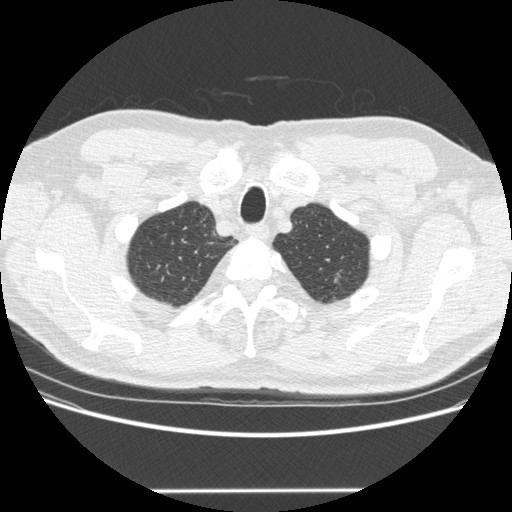
Low-dose screening chest CT, axial slice; second screening round (one year after baseline); lung window (W 1500 / L -600 HU); standard (soft-tissue) reconstruction kernel (STANDARD); 120 kVp; slice 45 of 223 in the series. Male participant, aged 69 years at enrolment.
- Expert reader's lesion annotation, bounding box (x1, y1, x2, y2) in pixels: (312, 263, 345, 293).
- Screening reader's record for this exam: no non-calcified nodule ≥4 mm recorded.
- Later outcome: lung cancer diagnosed 485 days after this screen — adenocarcinoma, NOS, left upper lobe, moderately differentiated (G2), stage IA (AJCC 6th edition), 10 mm at pathology.